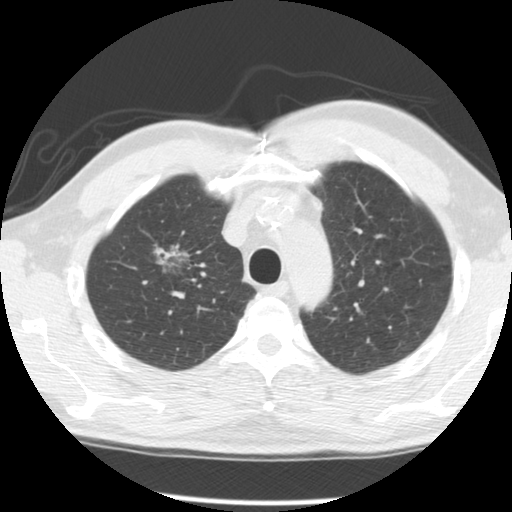
Chest CT (low-dose screening protocol), one axial image, second screening round (one year after baseline), lung window (W 1500 / L -600 HU), 2.5 mm slice thickness, standard (soft-tissue) reconstruction kernel (STANDARD), slice 25 of 120 in the series, 512 × 512 image matrix, field of view 340 × 340 mm. Male participant, aged 64 years at enrolment.
Expert-annotated lung lesion, bounding box <120,216,208,294> (left, top, right, bottom; pixels). The screening reader recorded 2 non-calcified nodules or masses ≥4 mm on this exam (right upper lobe, left upper lobe); which of them this box marks is not recorded. Official screen result: positive, other. Participant outcome: lung cancer diagnosed 429 days after this screen (after the third annual screen) — adenocarcinoma, NOS, right upper lobe, well differentiated (G1), stage IB (AJCC 6th edition), 45 mm at pathology.